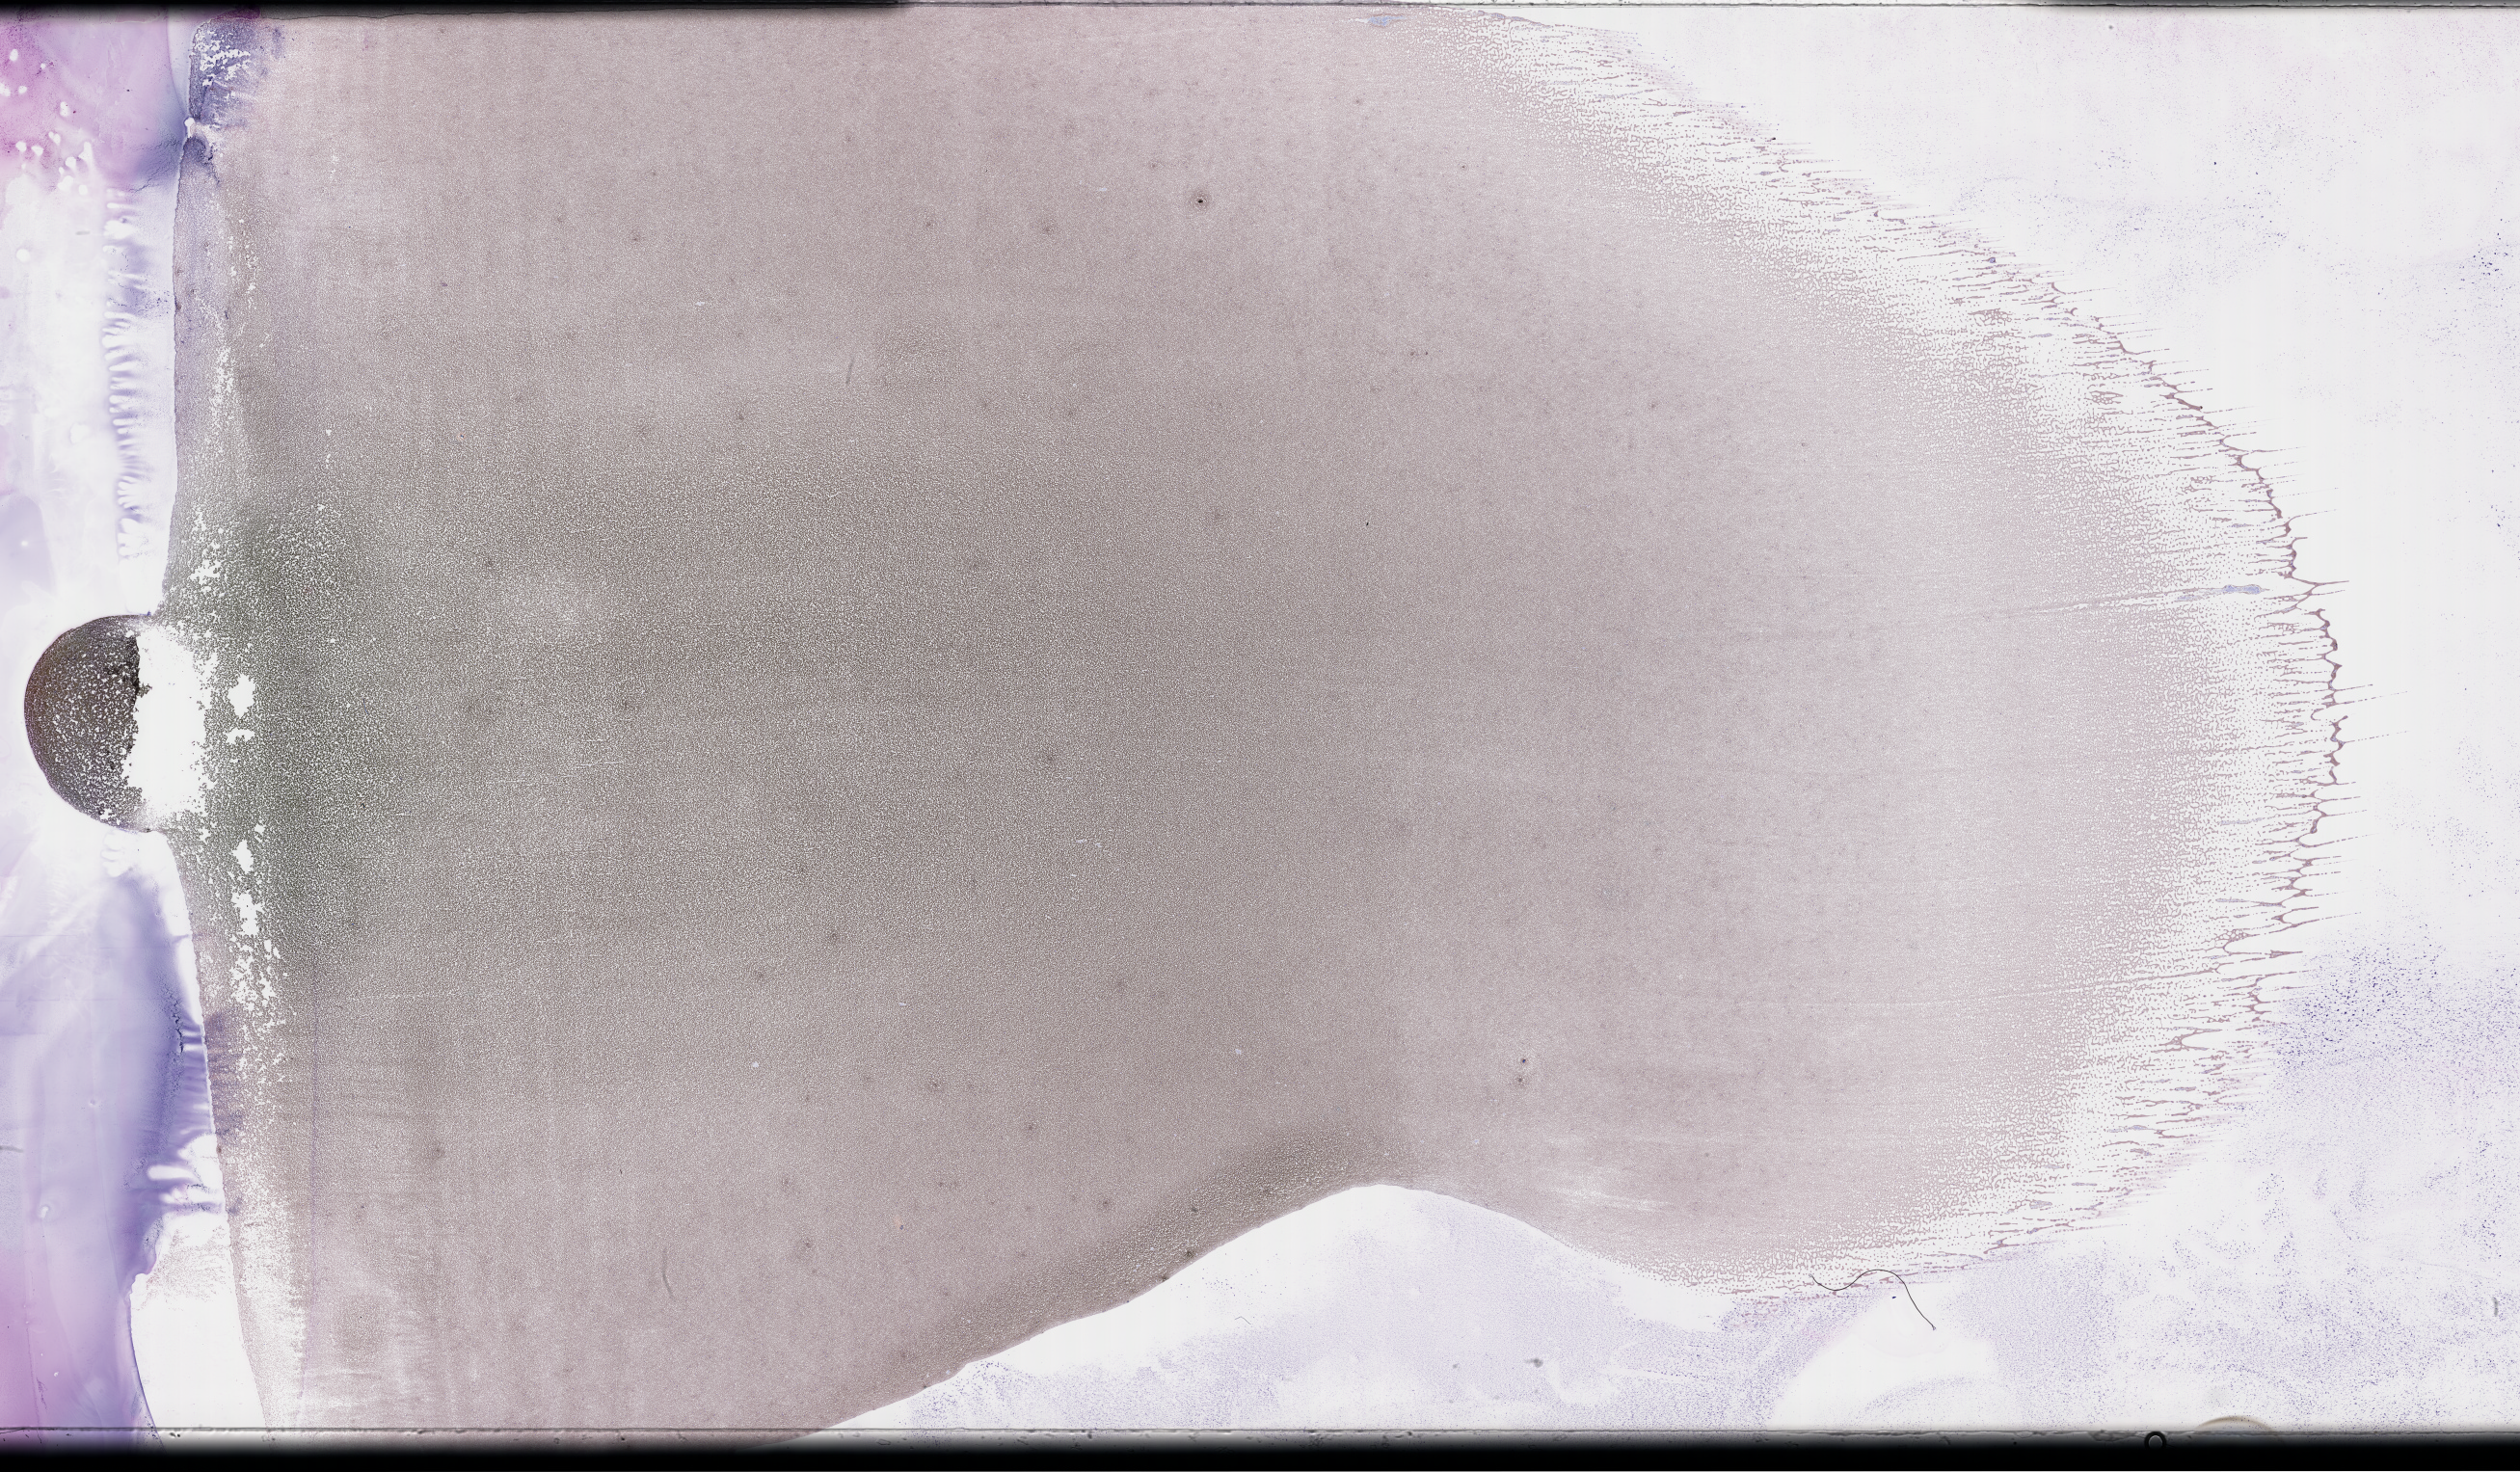
Whole-slide image of a whole blood smear, Wright-Giemsa stain, a low-resolution overview of the entire scanned area, about 42.2 x 24.7 mm, EDTA-anticoagulated smear, specimen time point: collected on treatment. Patient: female.
From a patient with: Plasma Cell Myeloma.